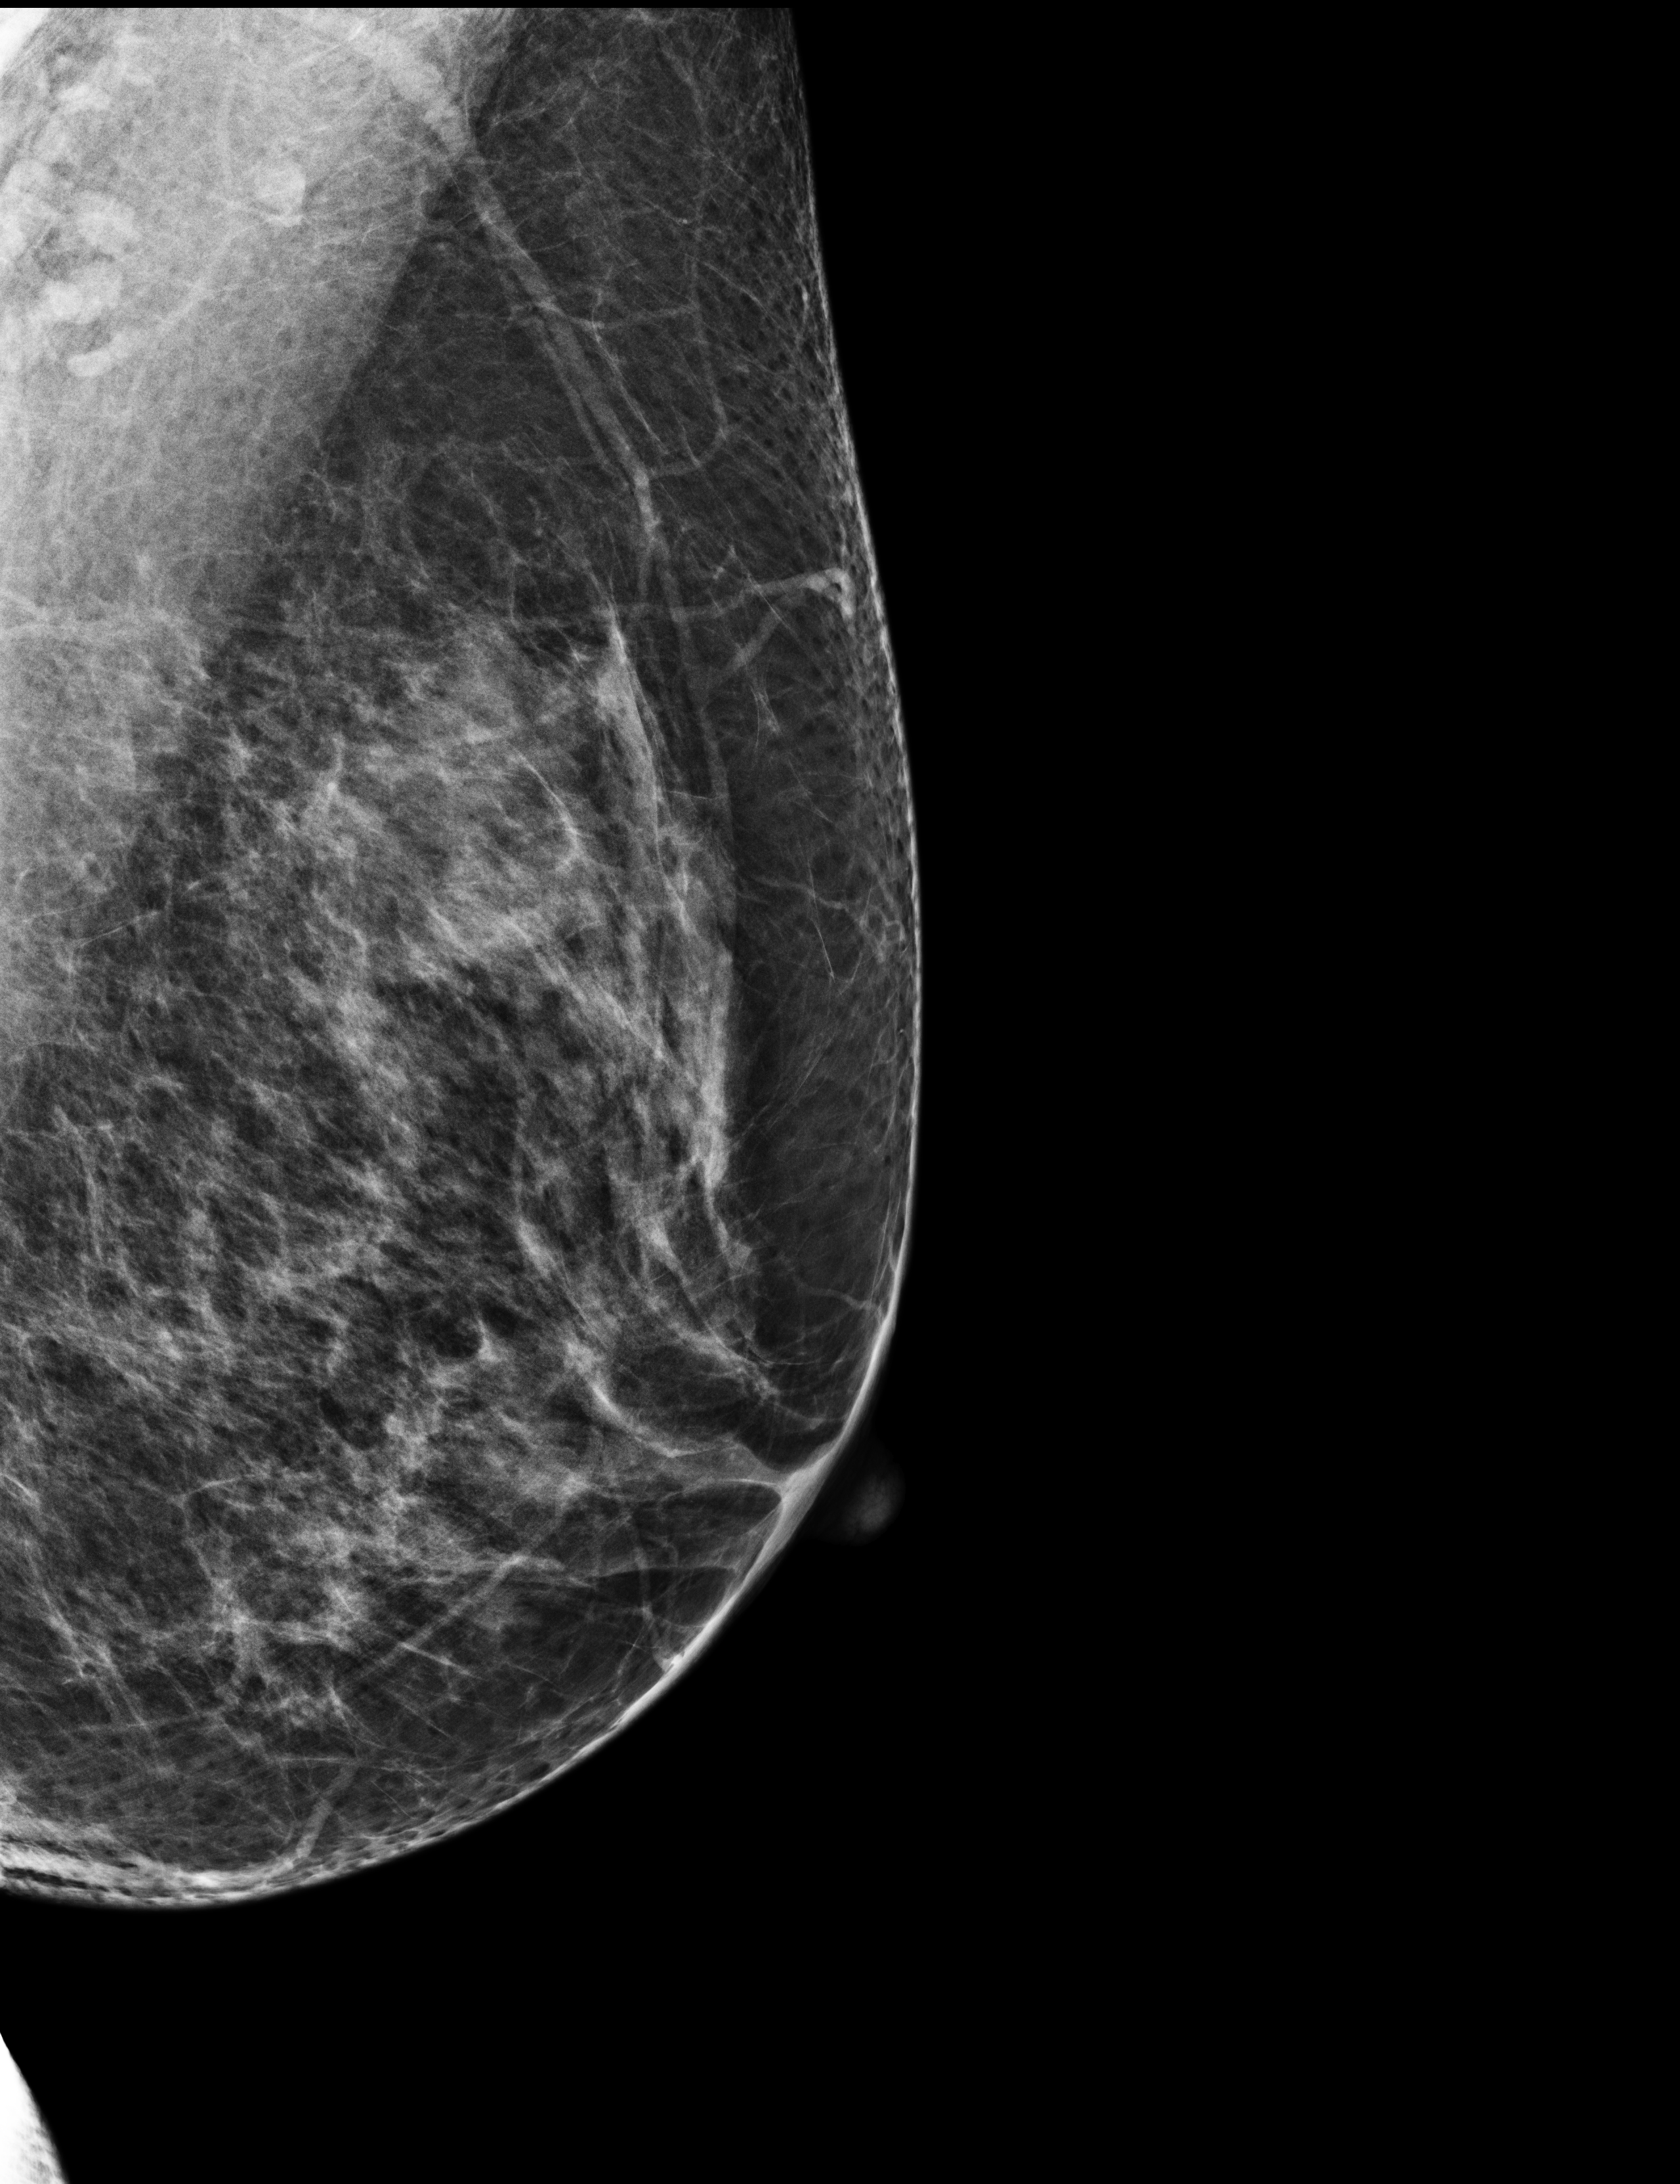
Screening examination; compressed breast thickness 68 mm; system: Selenia Dimensions. Female patient, age 54 years.
Image type: full-field digital mammogram. Breast: left. Projection: mediolateral oblique (MLO) view.